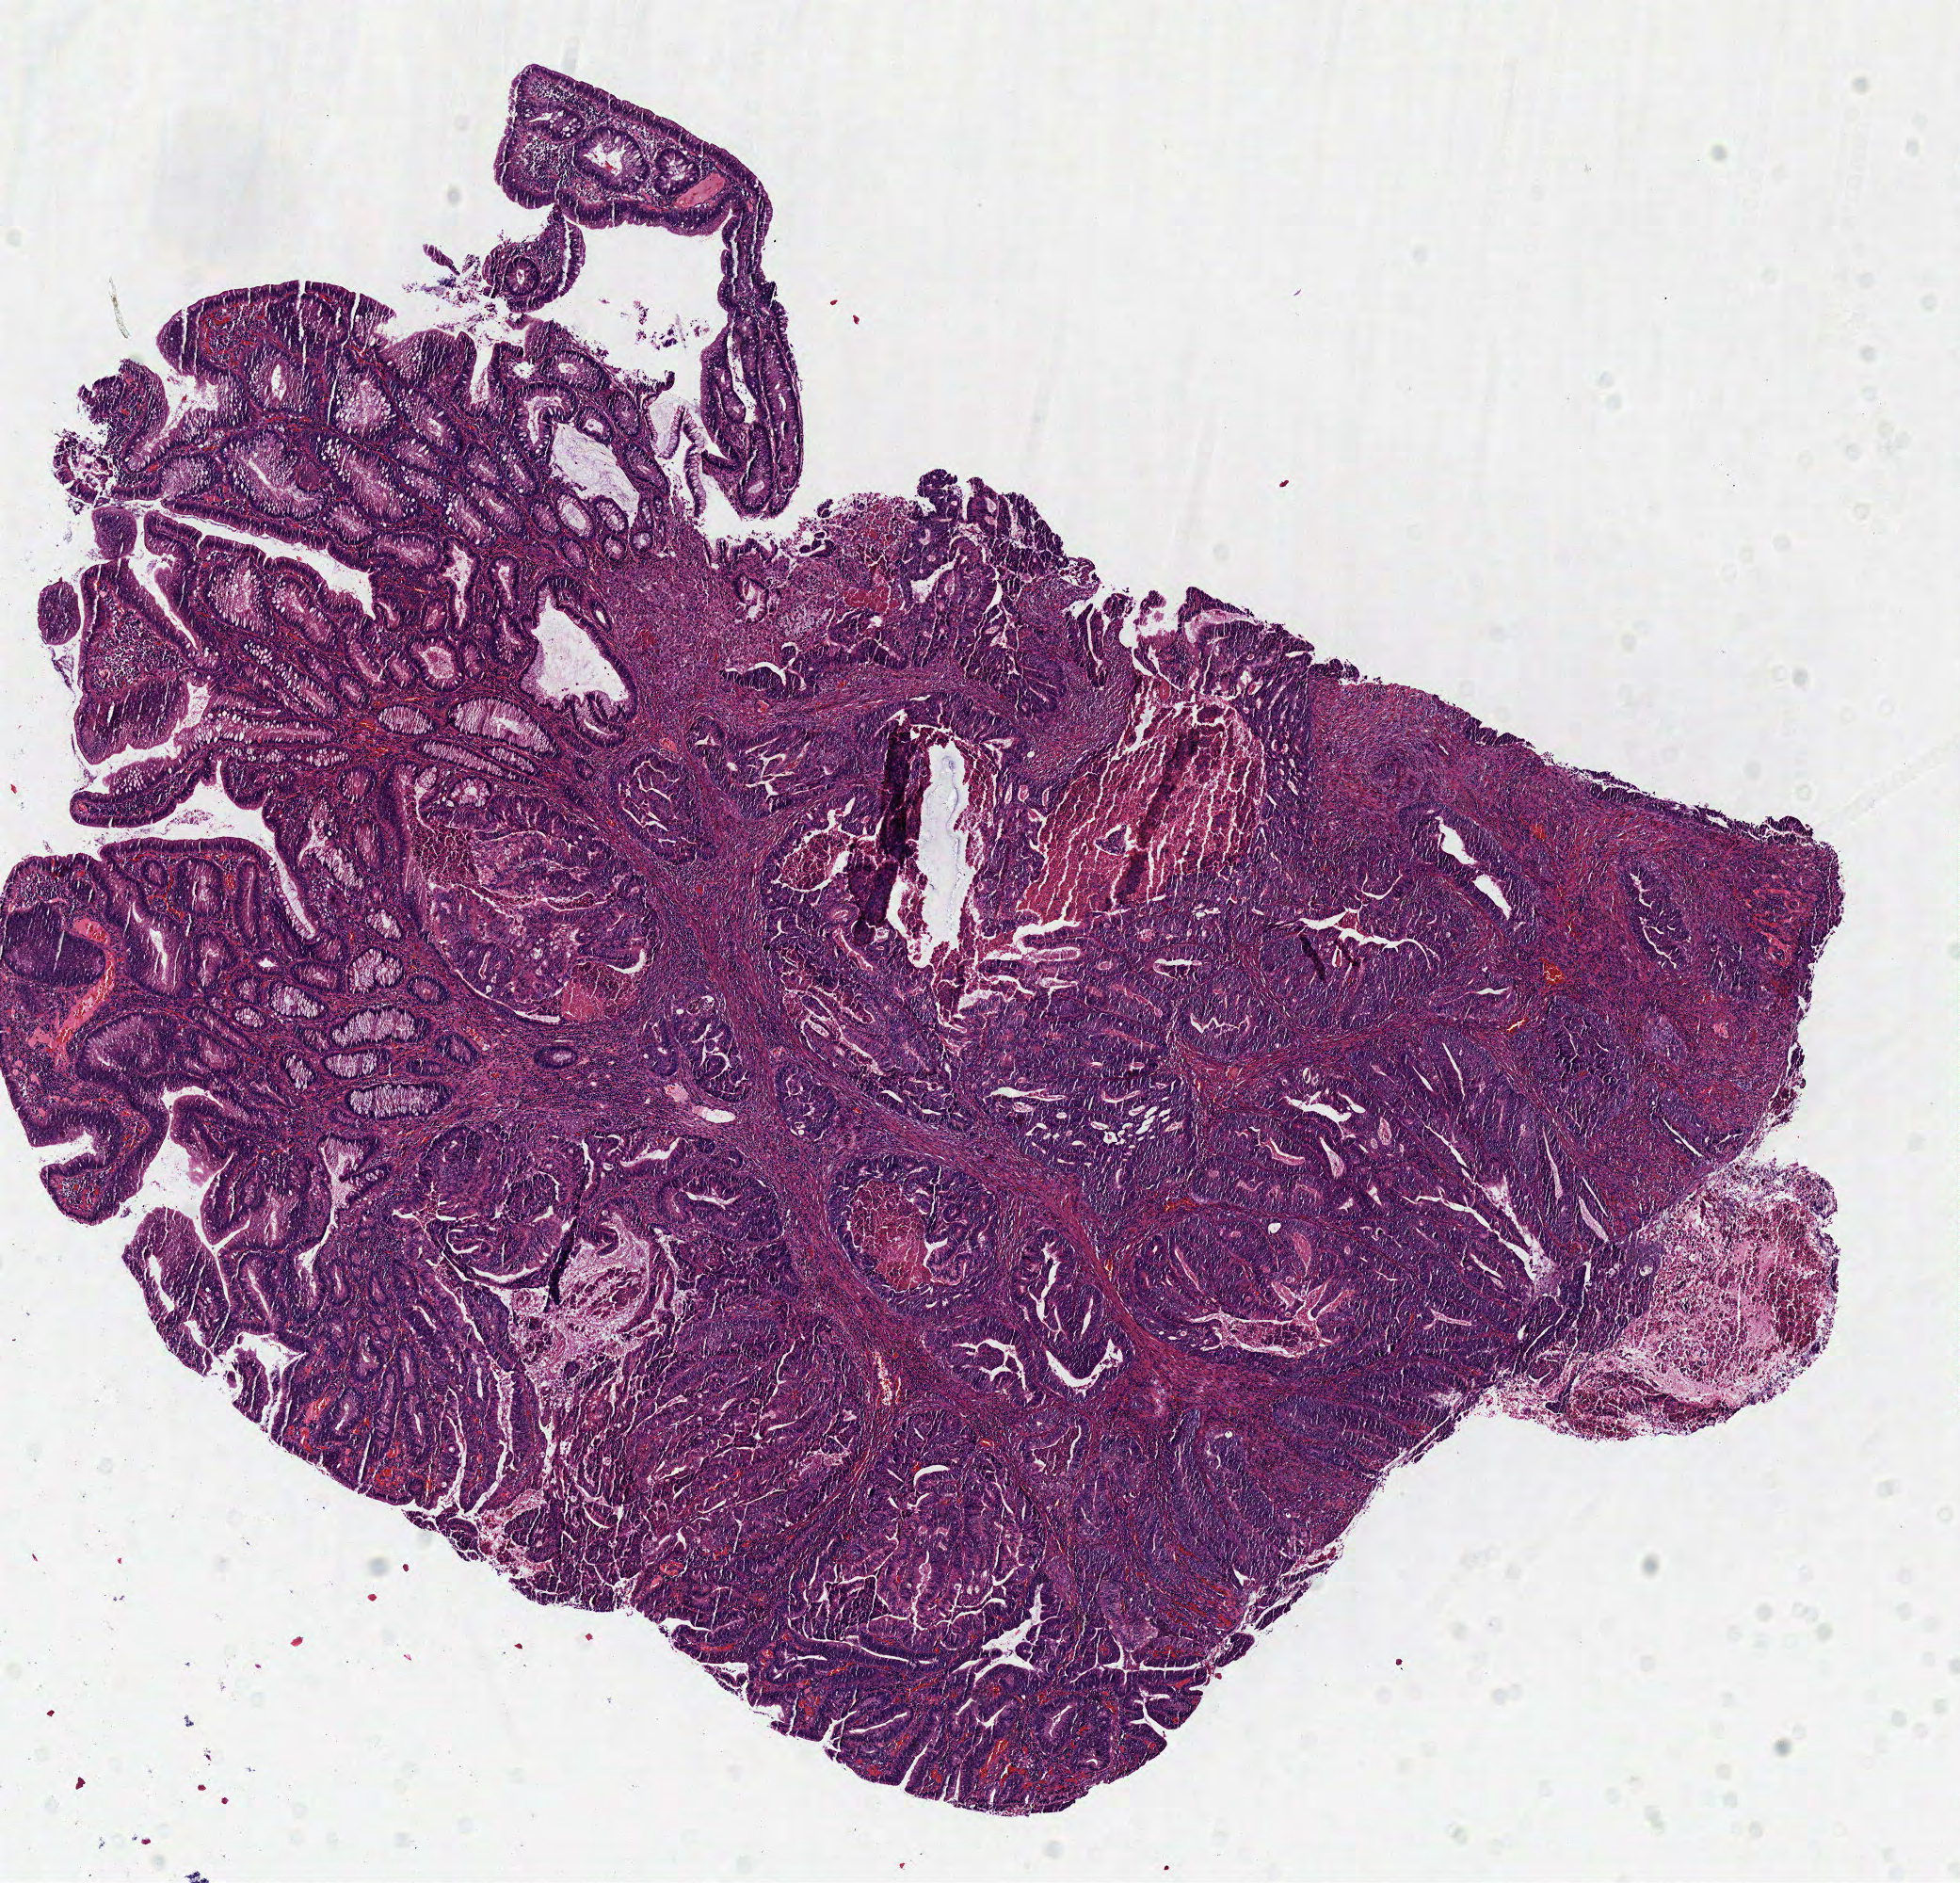
Whole-slide histology image, Hematoxylin and eosin (H&E) stained — whole scanned area (about 8.2 x 7.9 mm, from a 40x scan) shown as a low-resolution overview. Frozen section from the top of the tissue portion. Primary tumour sample from the colon. Patient: male, age at initial diagnosis 55 years. Slide review estimates, as recorded: tumour cells 90%, tumour nuclei 70%, normal cells 0%, stromal cells 0%, necrosis 10%. Infiltration values recorded for this section: lymphocyte infiltration 10%, monocyte infiltration 0%, neutrophil infiltration 10%.
Diagnosis: Adenocarcinoma, NOS. TNM: T3 N1c M0. AJCC pathologic stage: IIIB. Lymph nodes positive (case pathology): 0 of 21 examined.